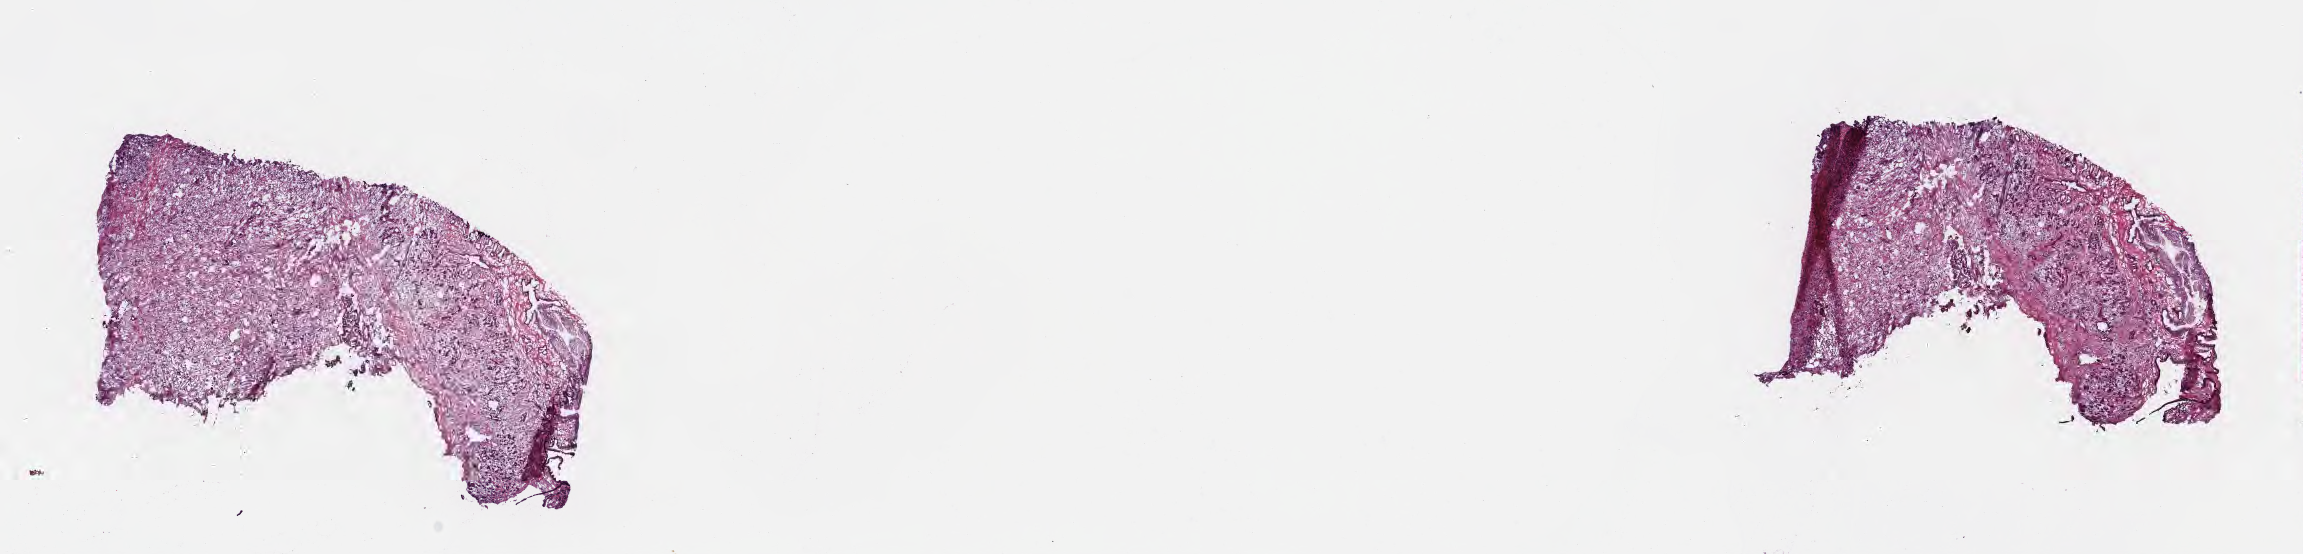
Digitized hematoxylin and eosin (H&E)-stained section — low-resolution overview of the scanned area, about 18.6 x 4.5 mm, cryosection, specimen: primary tumor, anatomic site: head of pancreas. Male, age 75 years at initial diagnosis. Tumor grade: G2 (moderately differentiated). Composition of this section per pathologist review: tumor cells 9%, tumor nuclei 13%, stromal cells 71%, necrosis 0%, normal cells 20%. Infiltration values recorded for this section: lymphocyte infiltration 40%, monocyte infiltration 3%, neutrophil infiltration 0%.
- AJCC pathologic stage: Stage III
- histologic diagnosis: Infiltrating duct carcinoma, NOS
- section: bottom of the tissue portion